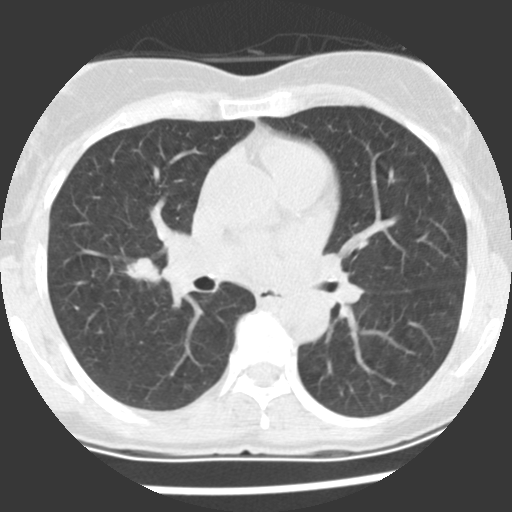
Low-dose screening chest CT, one axial slice; slice 121 of 225 in the series (ordered by position); lung window (W 1500 / L -600 HU); 512 × 512 image matrix, field of view 270 × 270 mm.
Annotated regions visible in this slice (outlined manually by an expert reader):
- lesion 1 (tumor, upper lobe of right lung): bounding box <127,258,161,283> (left, top, right, bottom; pixels)